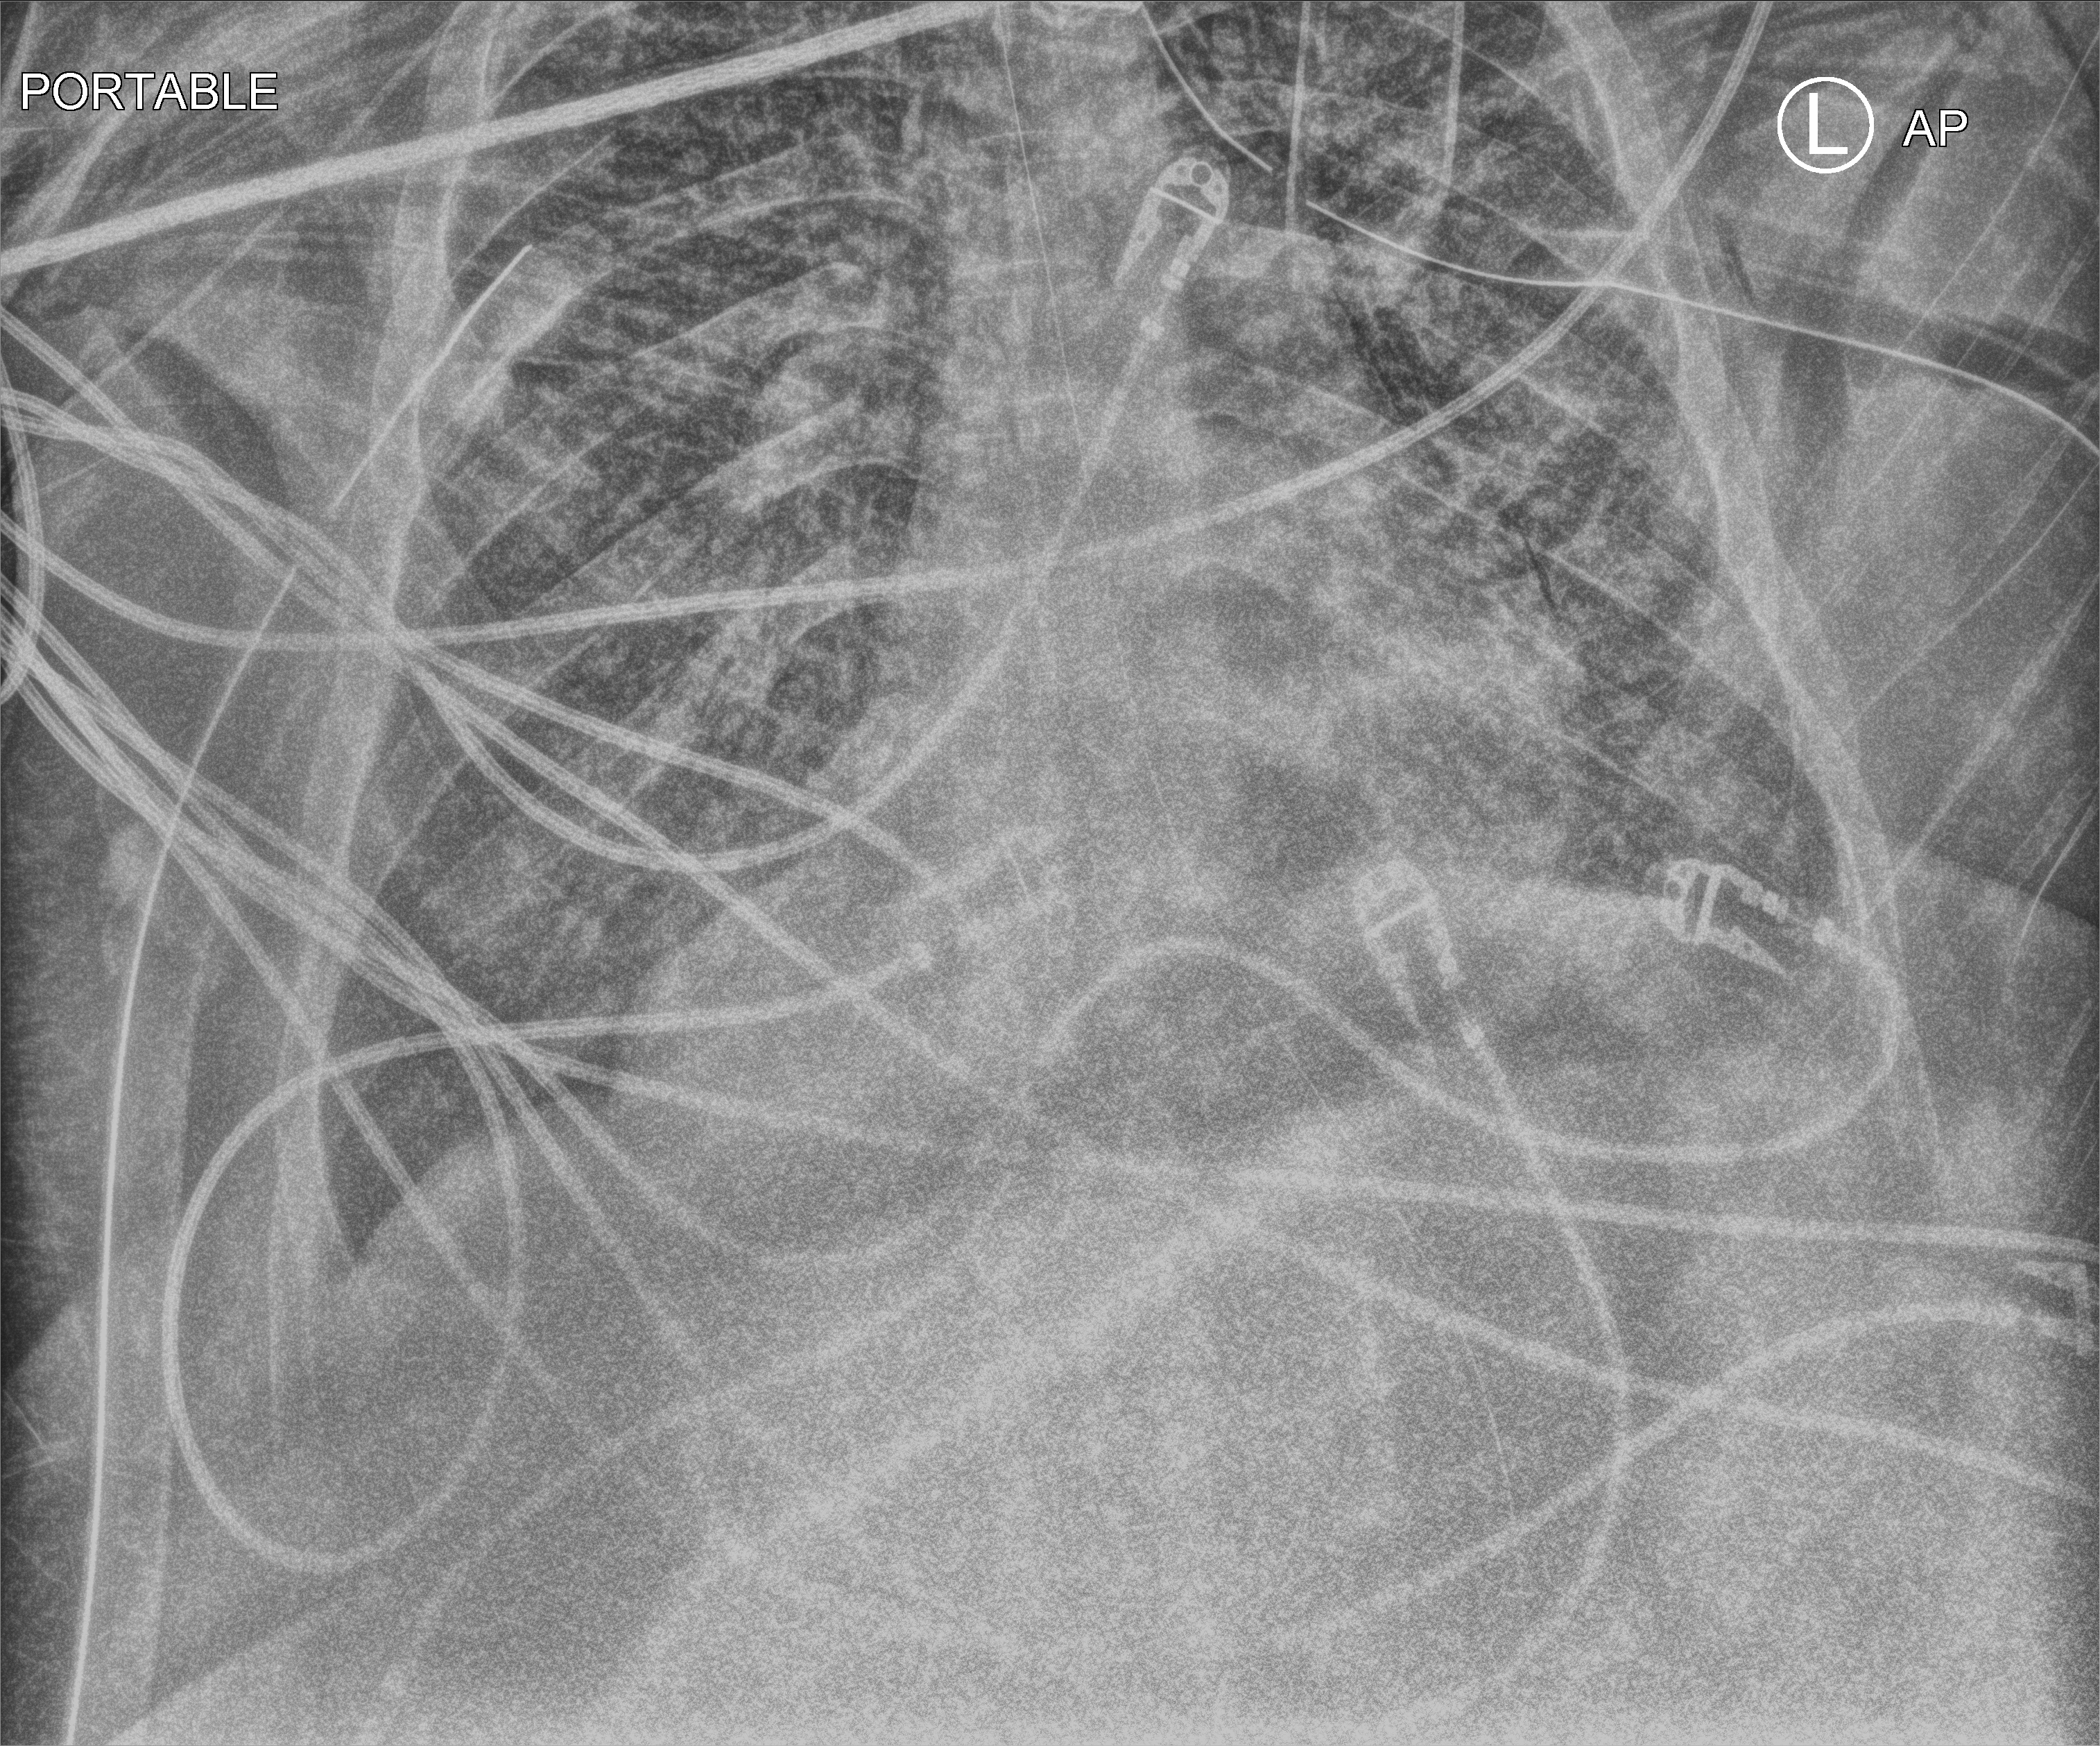
Portable chest radiograph, anteroposterior (AP) projection. Adult patient hospitalised with COVID-19, age 18–59 years.
Admission-level facts for this patient (not findings on this image; timing relative to this image not recorded):
- mechanically ventilated during this hospital stay: yes